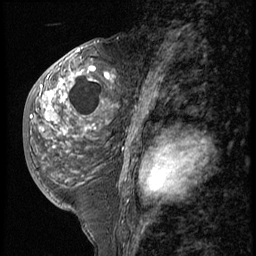
Breast MRI (dynamic contrast-enhanced), one sagittal slice; position 30 of 56 along the scan axis; 3 images stored at this slice position (order not interpretable as contrast timing); 1.5 T; TE 4.2 ms, TR 9 ms; 2.5 mm slice thickness; 256 × 256 image matrix. Female patient, age 50 years. From the clinical record (not read from this slice): setting: breast cancer imaged before/during neoadjuvant chemotherapy; receptor status: triple-negative.
Structures marked on this image (semi-automatically segmented with operator editing):
- analysis volume of interest (the breast-tissue region the enhancement analysis was run in; not a lesion): bounding box <25,50,118,191> (left, top, right, bottom; pixels)
- tumour enhancement mask (voxels above the 140 % enhancement threshold inside the analysis volume of interest): <31,50,115,131>